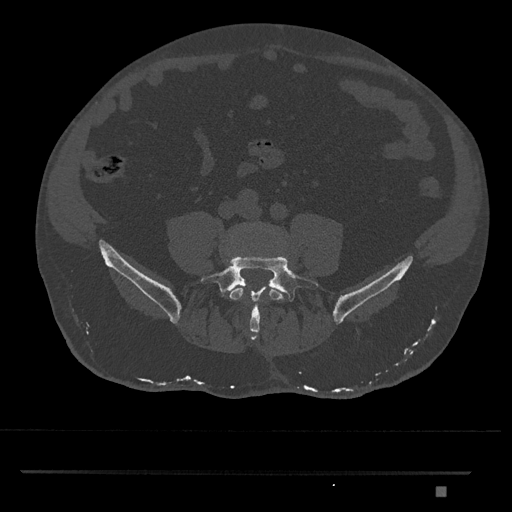
CT including the spine, one axial slice; position 574 of 1134 along the scan axis; reconstruction kernel Br40s/3; bone window (W 1800 / L 400 HU); 512 × 512 image matrix, field of view 429 × 429 mm. Patient: male, 65 years. Case-level facts recorded for this patient, not image findings: primary cancer: prostate.
Annotated regions visible in this slice (semi-automatic segmentation, software-assisted and operator-edited):
- L4 vertebra: box from (x=229, y=222) to (x=285, y=301) px
- L5 vertebra: (x=200, y=255)–(x=322, y=334)